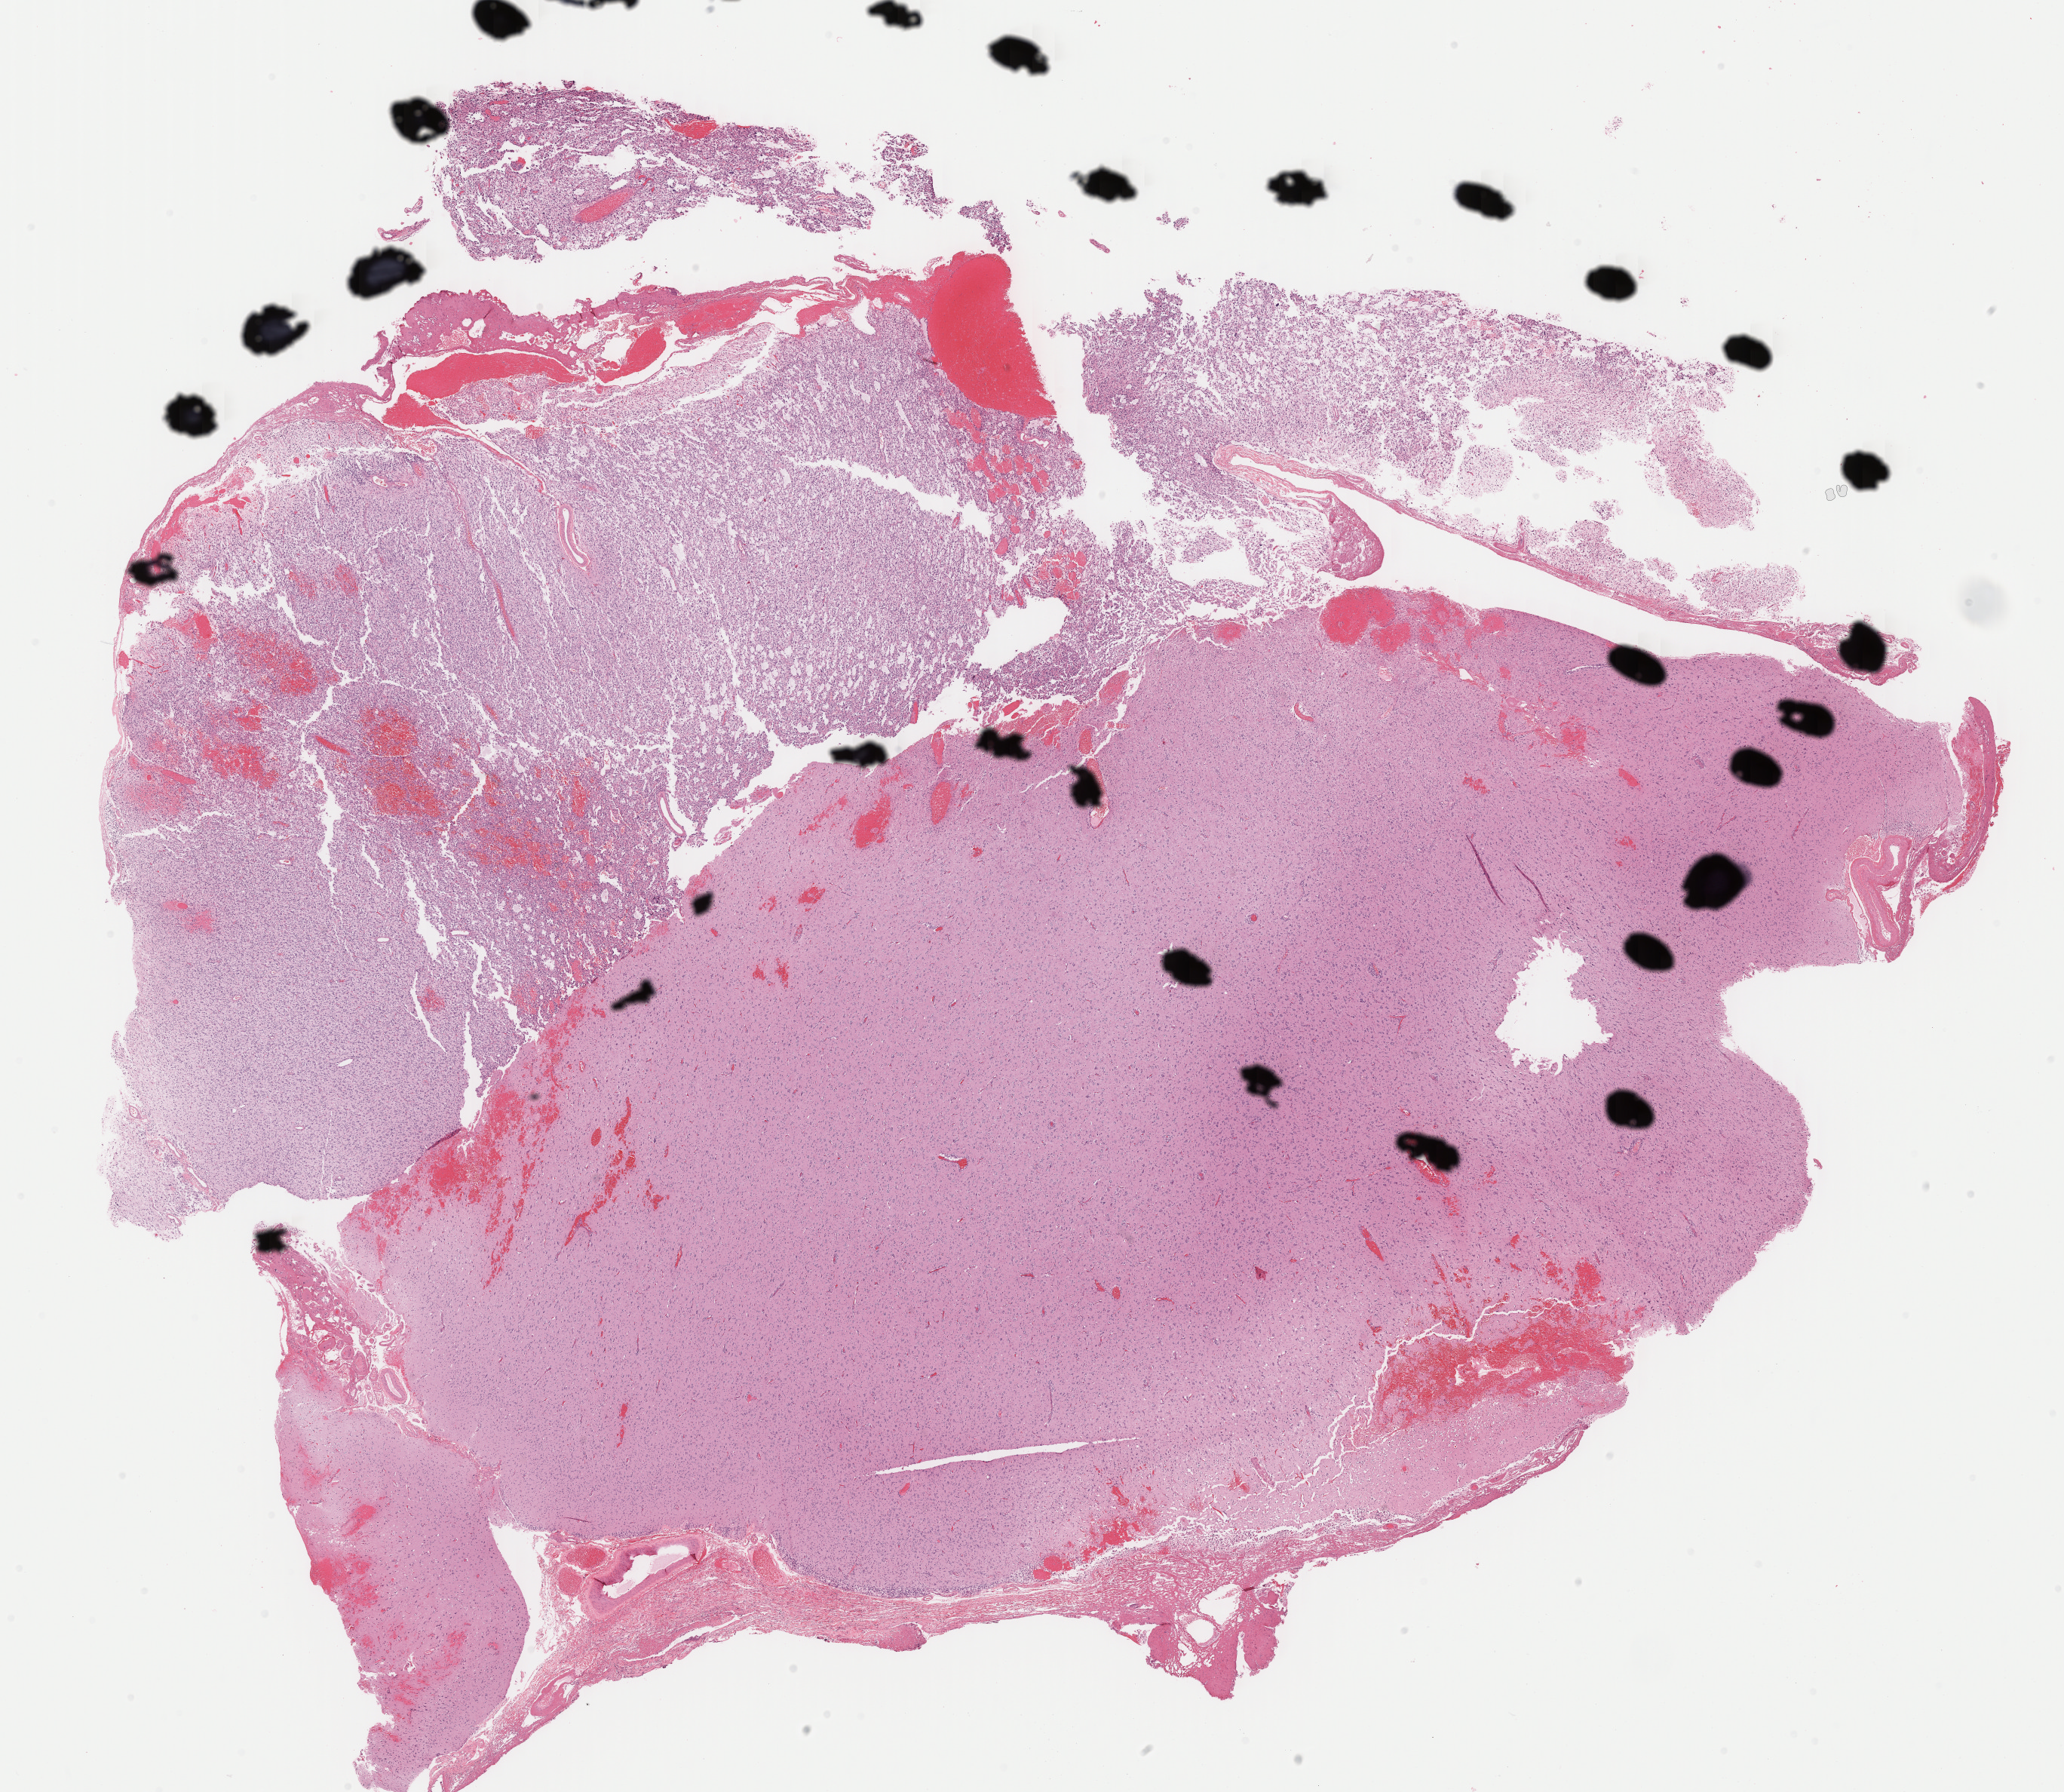
Digitized H&E tissue section (whole slide) — whole scanned area (about 21.6 x 18.7 mm) shown as a low-resolution overview. Formalin-fixed paraffin-embedded (FFPE) diagnostic section. Sample: primary tumour, brain. Patient: male, age at initial diagnosis 34 years. Histologic grade: G3 (poorly differentiated).
Laterality: left. Histologic diagnosis: Astrocytoma, anaplastic (cerebrum).